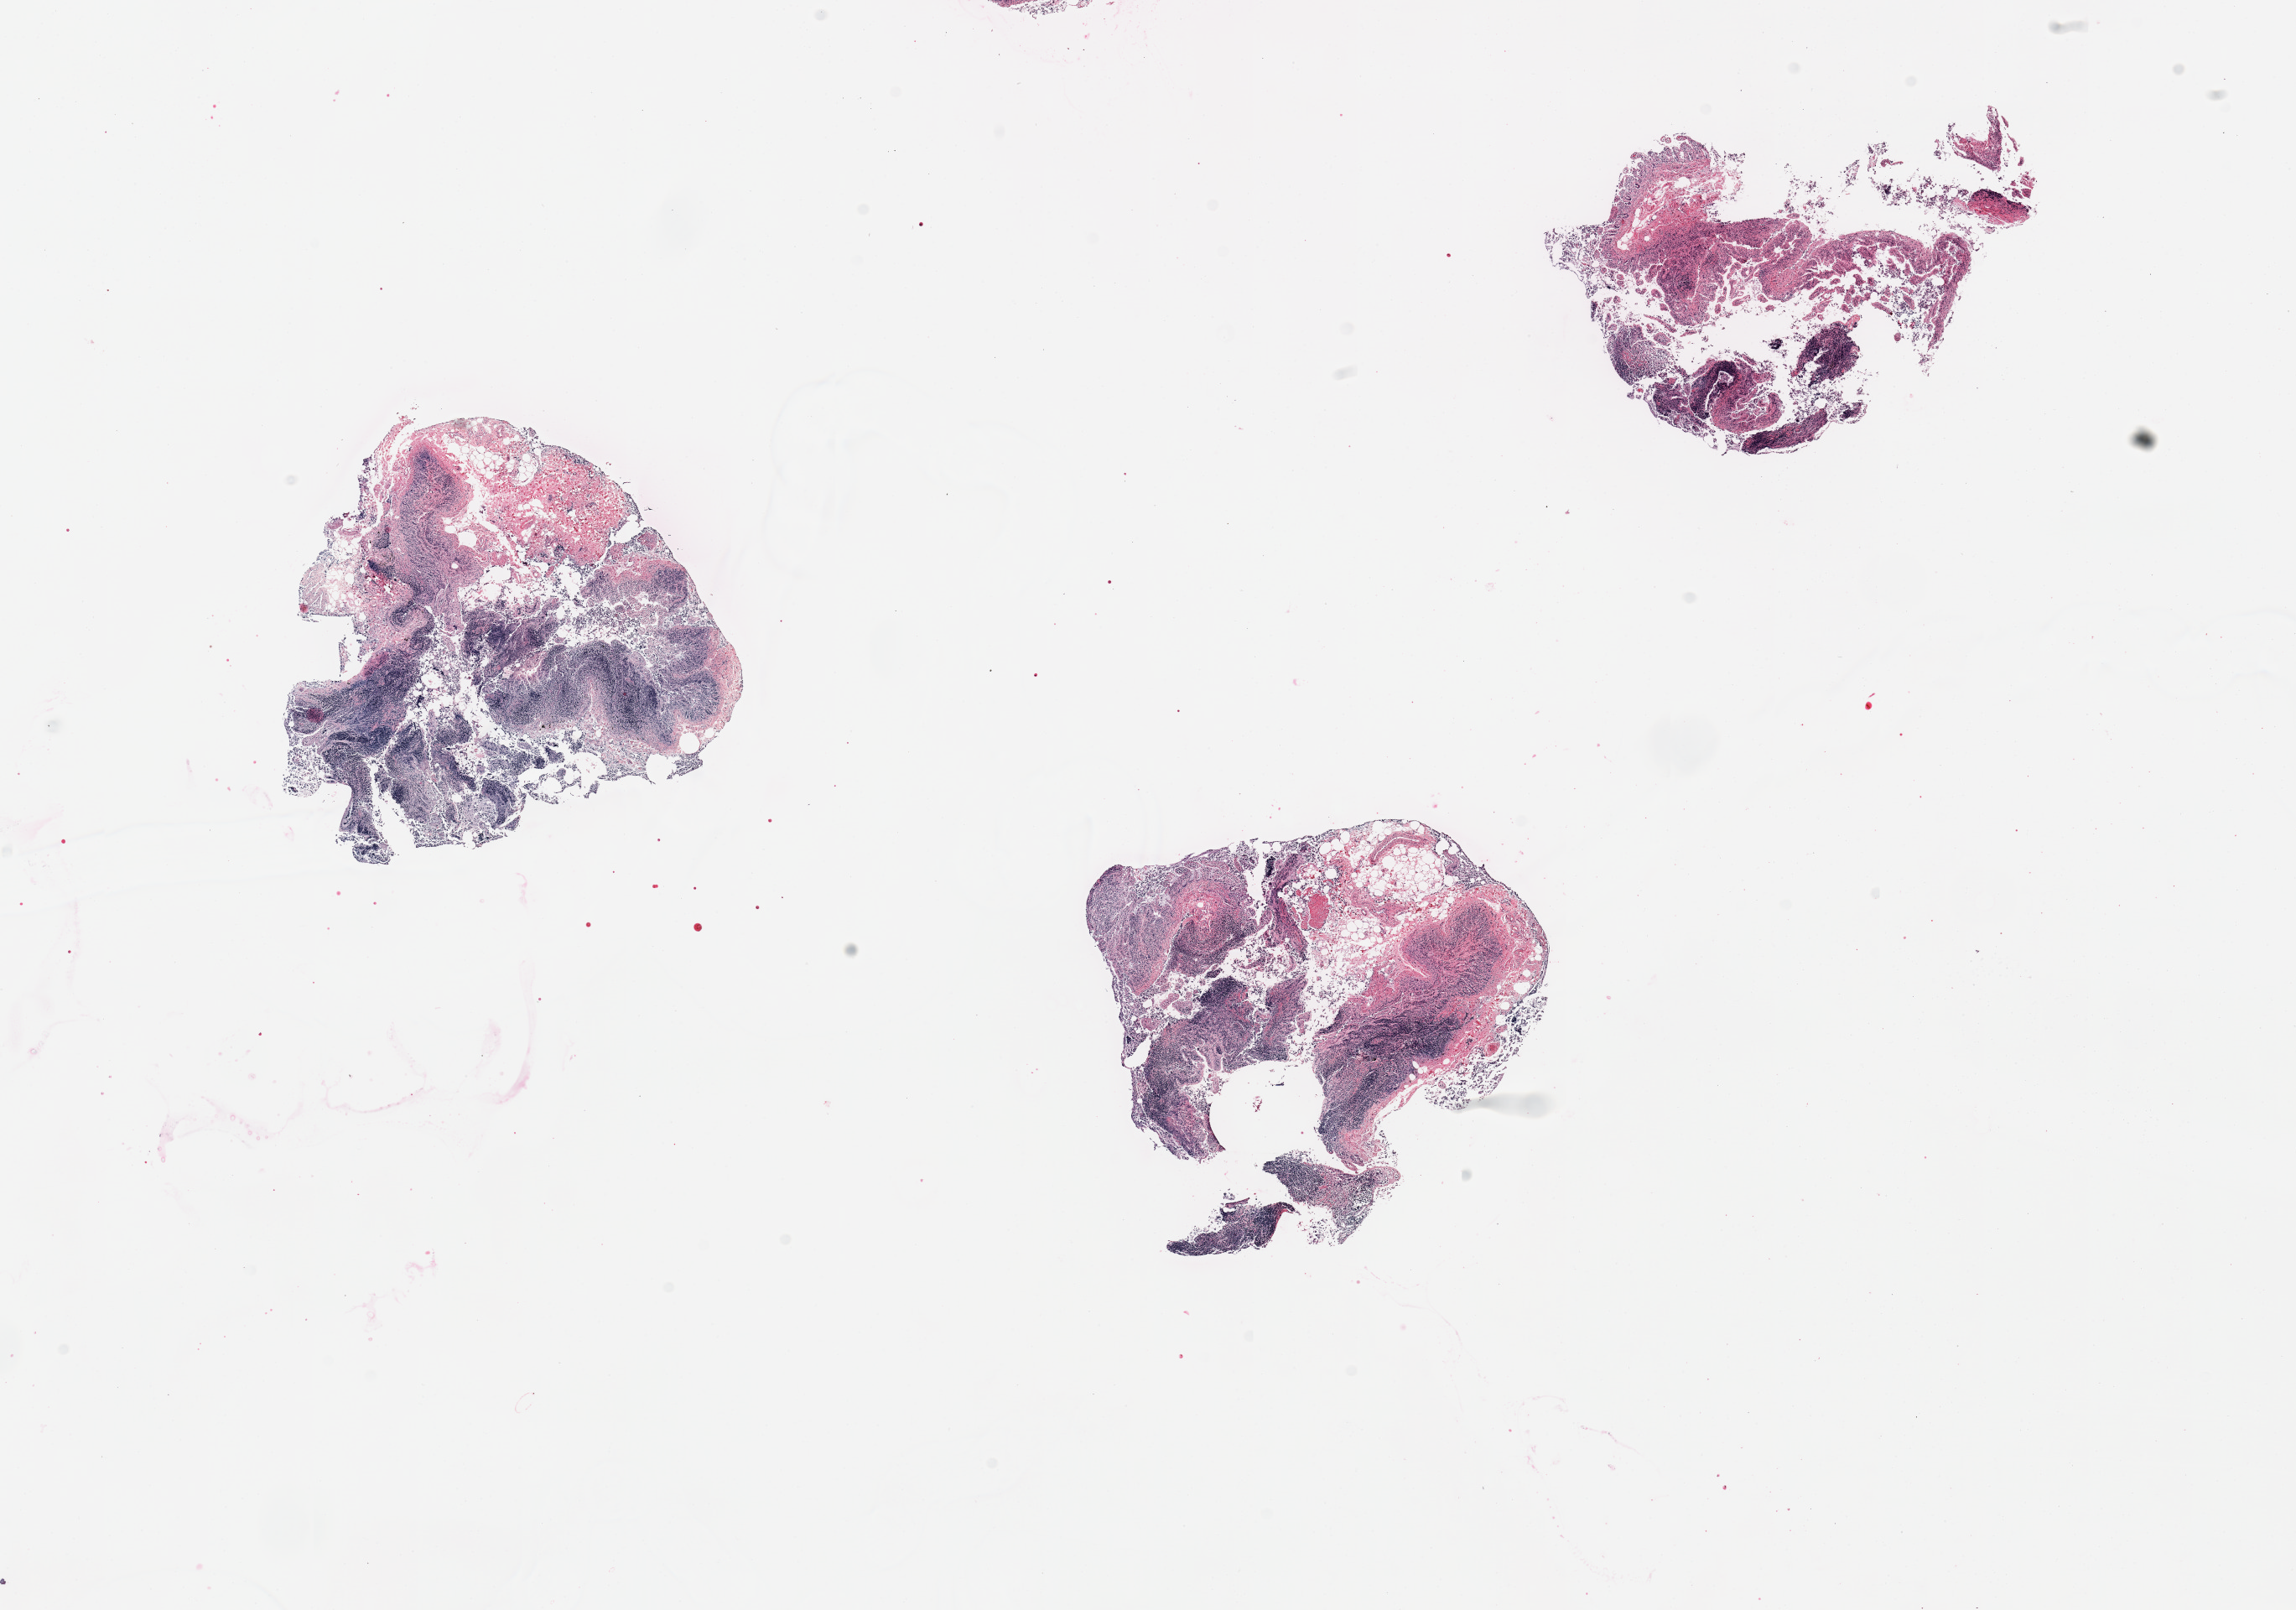
Whole-slide image, hematoxylin and eosin (H&E) stain, brightfield, low-resolution overview of the scanned area, about 21.7 x 15.2 mm (acquisition: 20x scan), PAXgene-fixed, paraffin-embedded tissue, sampled site (target tissue): ileum, donor tissue sample. Male donor.
• pathologist's review note for this sample: 3 pieces, ~50-60% lymphoid aggregates; mucosal elements largely sloughed/autolyzed